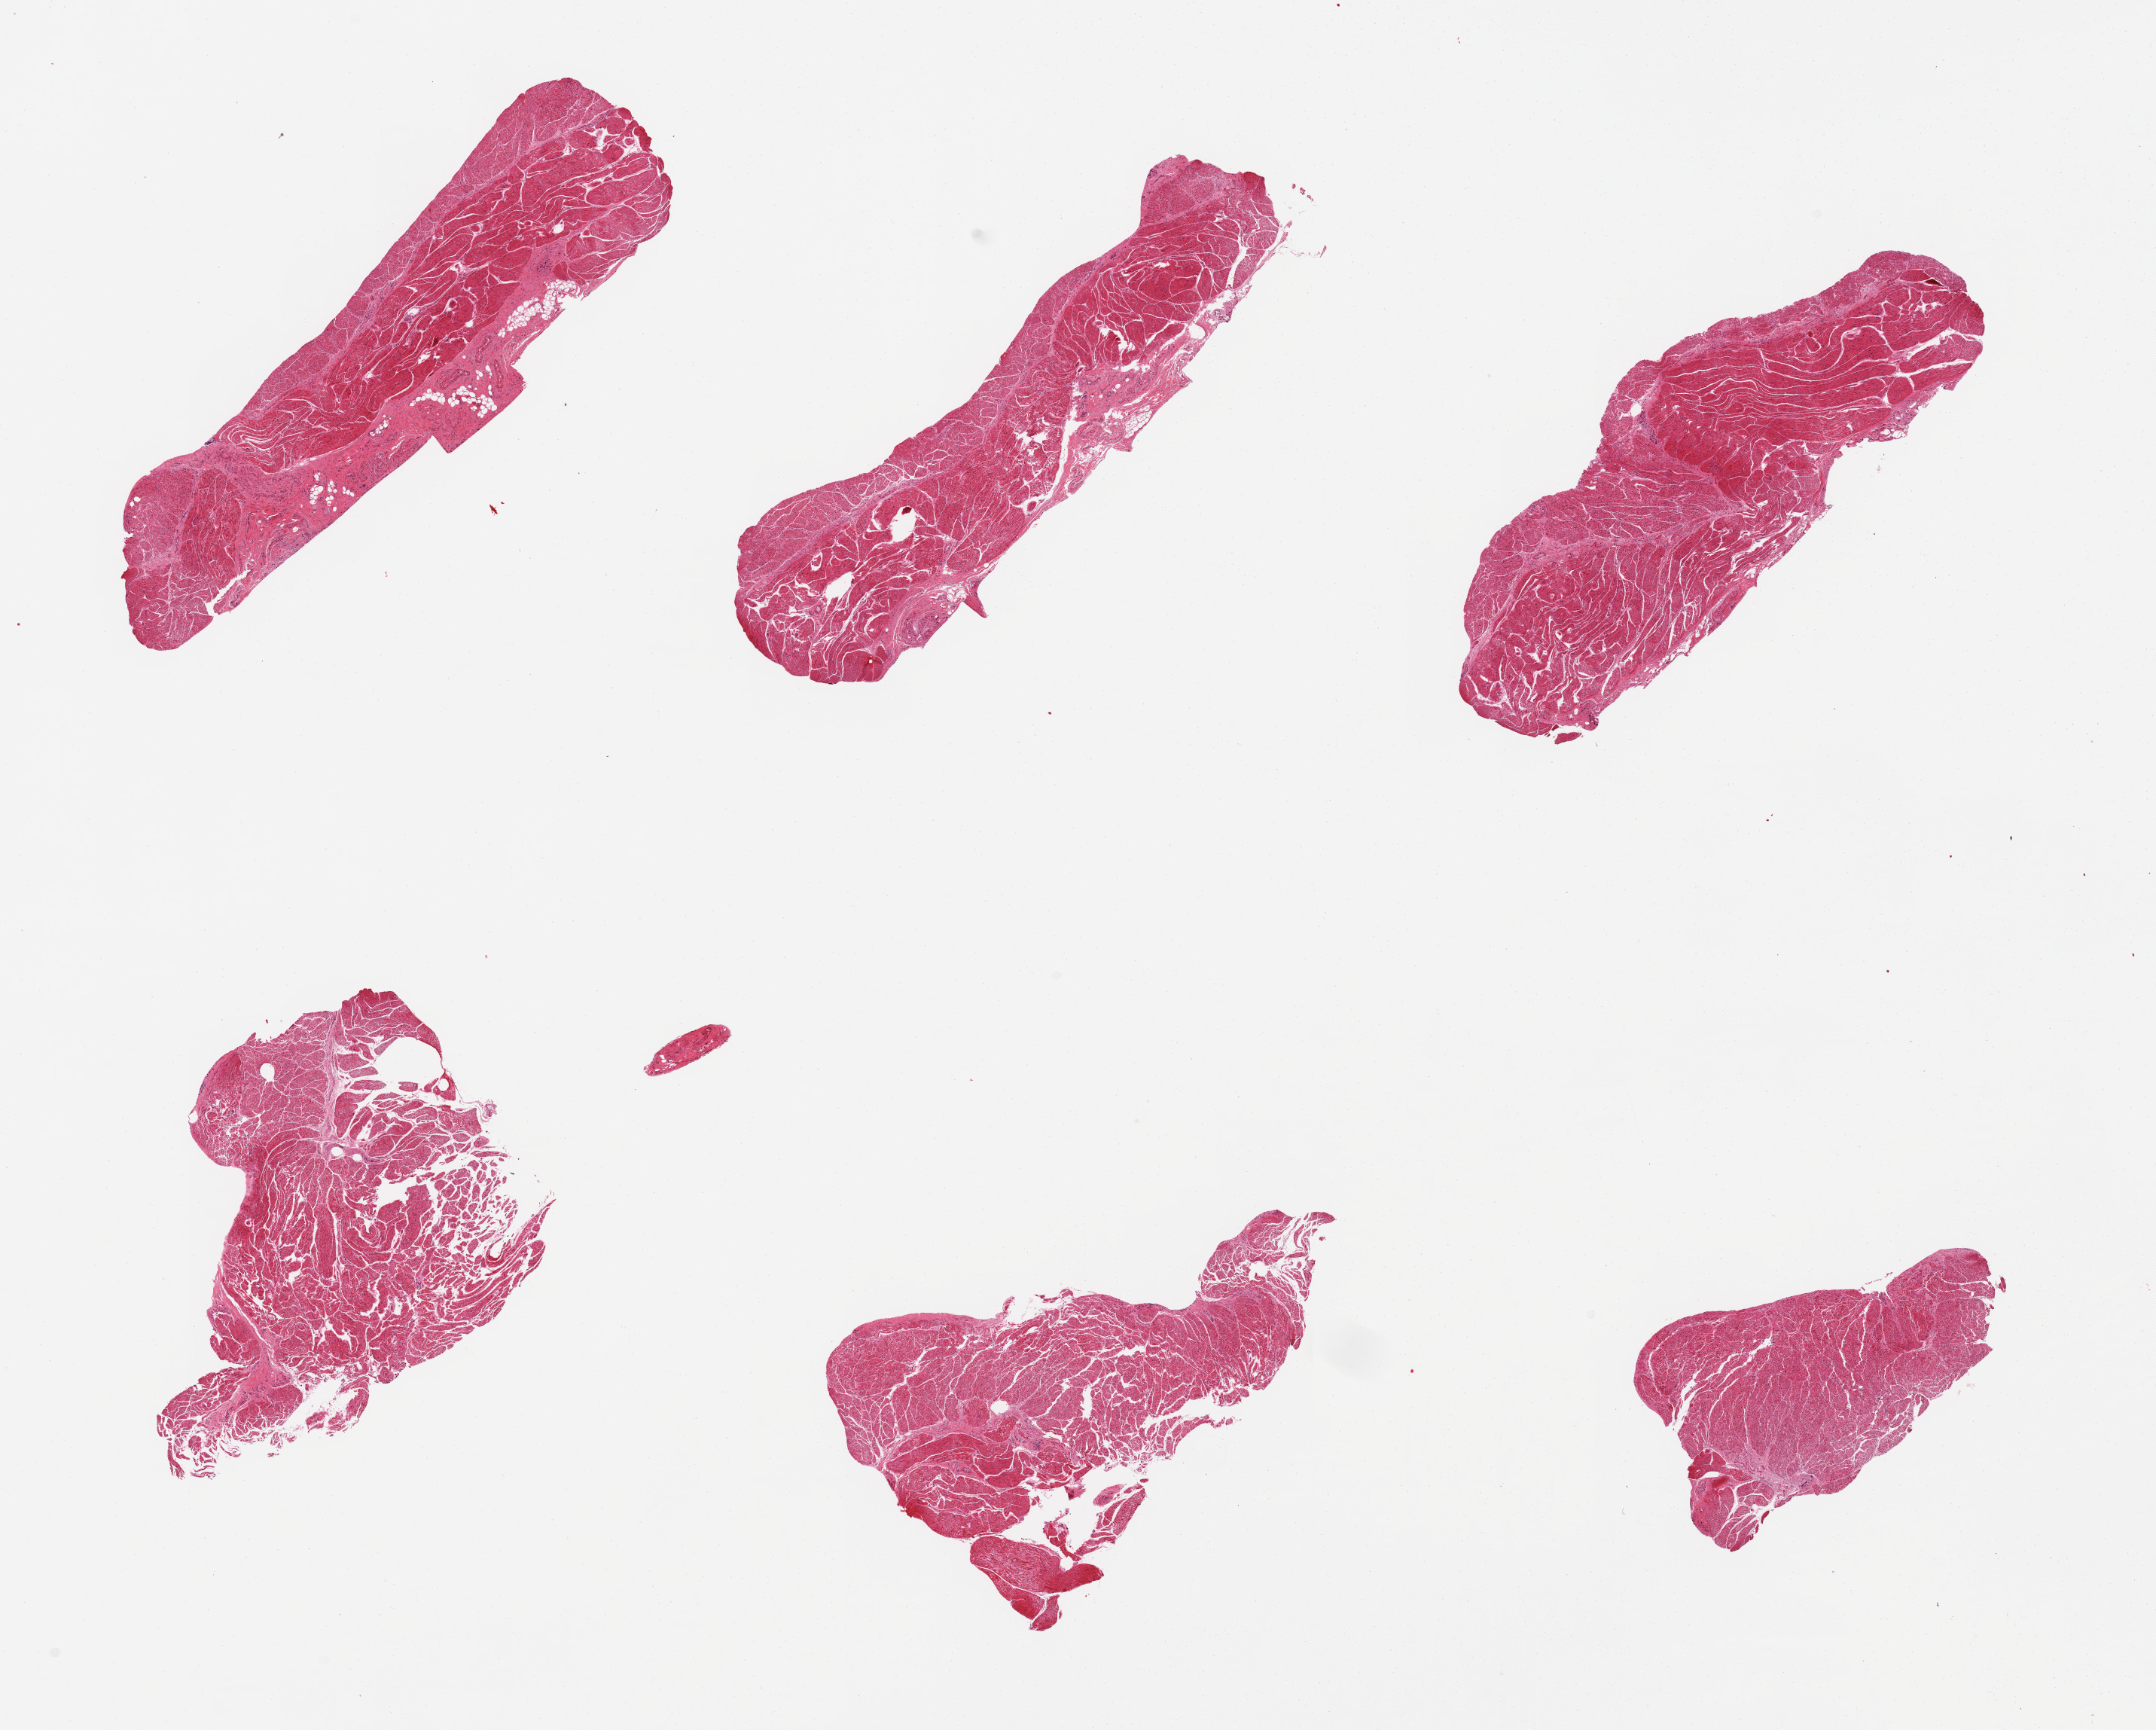
Whole-slide image, H&E stain, brightfield — whole scanned area (about 22.6 x 18.2 mm) shown as a low-resolution overview; PAXgene-fixed, paraffin-embedded tissue; section of esophageal muscle (target tissue); tissue donor sample. Donor: male.
Review note (as recorded): 6 pieces, well trimmed.